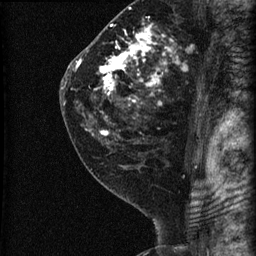
Breast MRI (dynamic contrast-enhanced), one sagittal slice. Position 43 of 60 along the scan axis. Dynamic contrast-enhanced series, image 2 of 3 at this slice position (ordered by acquisition). 1.5 T. TE 4.2 ms, TR 22.7 ms. 1.8 mm slice thickness. 256 × 256 image matrix, field of view 180 × 180 mm. Female patient, age 45 years. From the clinical record (not read from this slice): setting: breast cancer imaged before/during neoadjuvant chemotherapy; receptor status: HR-positive, HER2-negative.
Outlined on this slice (semi-automatically segmented with operator editing):
- analysis volume of interest (the breast-tissue region the enhancement analysis was run in; not a lesion): box from (x=74, y=11) to (x=205, y=140) px
- tumour enhancement mask (voxels above the 90 % enhancement threshold inside the analysis volume of interest): (x=76, y=23)–(x=175, y=135)